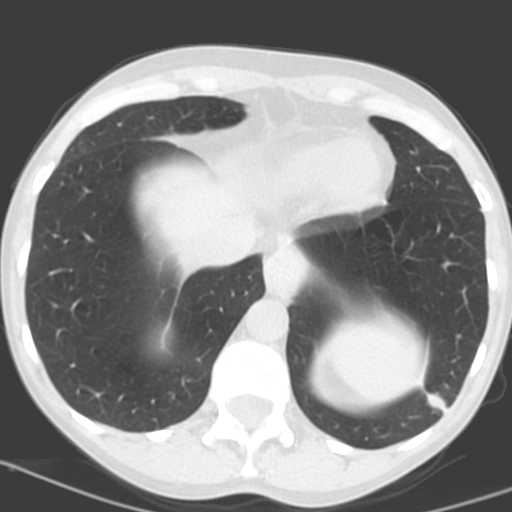
Low-dose screening chest CT, one axial slice. Slice 39 of 156 in the series (ordered by position). Lung window (W 1500 / L -600 HU). 3.2 mm slice thickness. 512 × 512 image matrix, field of view 262 × 262 mm.
Outlined on this slice (outlined manually by an expert reader):
- lesion 1 (tumor, lower lobe of left lung): bounding box <427,393,447,413> (left, top, right, bottom; pixels)